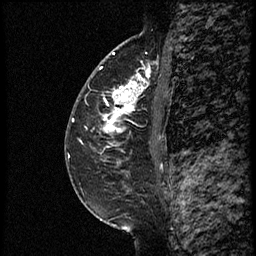
Breast MRI (dynamic contrast-enhanced), one sagittal slice. Position 37 of 60 along the scan axis. Dynamic contrast-enhanced study with each time point stored as its own series, time point 2 of 3 at this slice position (early post-contrast, ordered by acquisition time). 1.5 T. TE 4.2 ms, TR 18.9 ms. 2 mm slice thickness. 256 × 256 image matrix. Female patient. Case-level facts recorded for this patient, not image findings: setting: breast cancer imaged before/during neoadjuvant chemotherapy; receptor status: HER2-positive.
Outlined on this slice (semi-automatically segmented with operator editing):
- analysis volume of interest (the breast-tissue region the enhancement analysis was run in; not a lesion): bounding box [x1, y1, x2, y2] px = [82, 64, 161, 147]
- tumour enhancement mask (voxels above the 100 % enhancement threshold inside the analysis volume of interest): [93, 72, 150, 134]